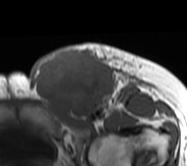
MRI of an extremity soft-tissue mass, one axial slice. MR volume resampled by the dataset authors to the PET/CT grid (not the native acquisition matrix). 187 × 166 image matrix, field of view 183 × 162 mm. Female patient. Case-level facts recorded for this patient, not image findings: histological type: leiomyosarcoma; grade: high; site of the primary tumour: groin.
Annotated regions visible in this slice (expert contour drawn on MRI and transferred to this co-registered scan by the dataset authors):
- gross tumour volume including surrounding oedema: bounding box <29,42,154,120> (left, top, right, bottom; pixels)
- gross tumour volume (mass): <30,46,115,120>